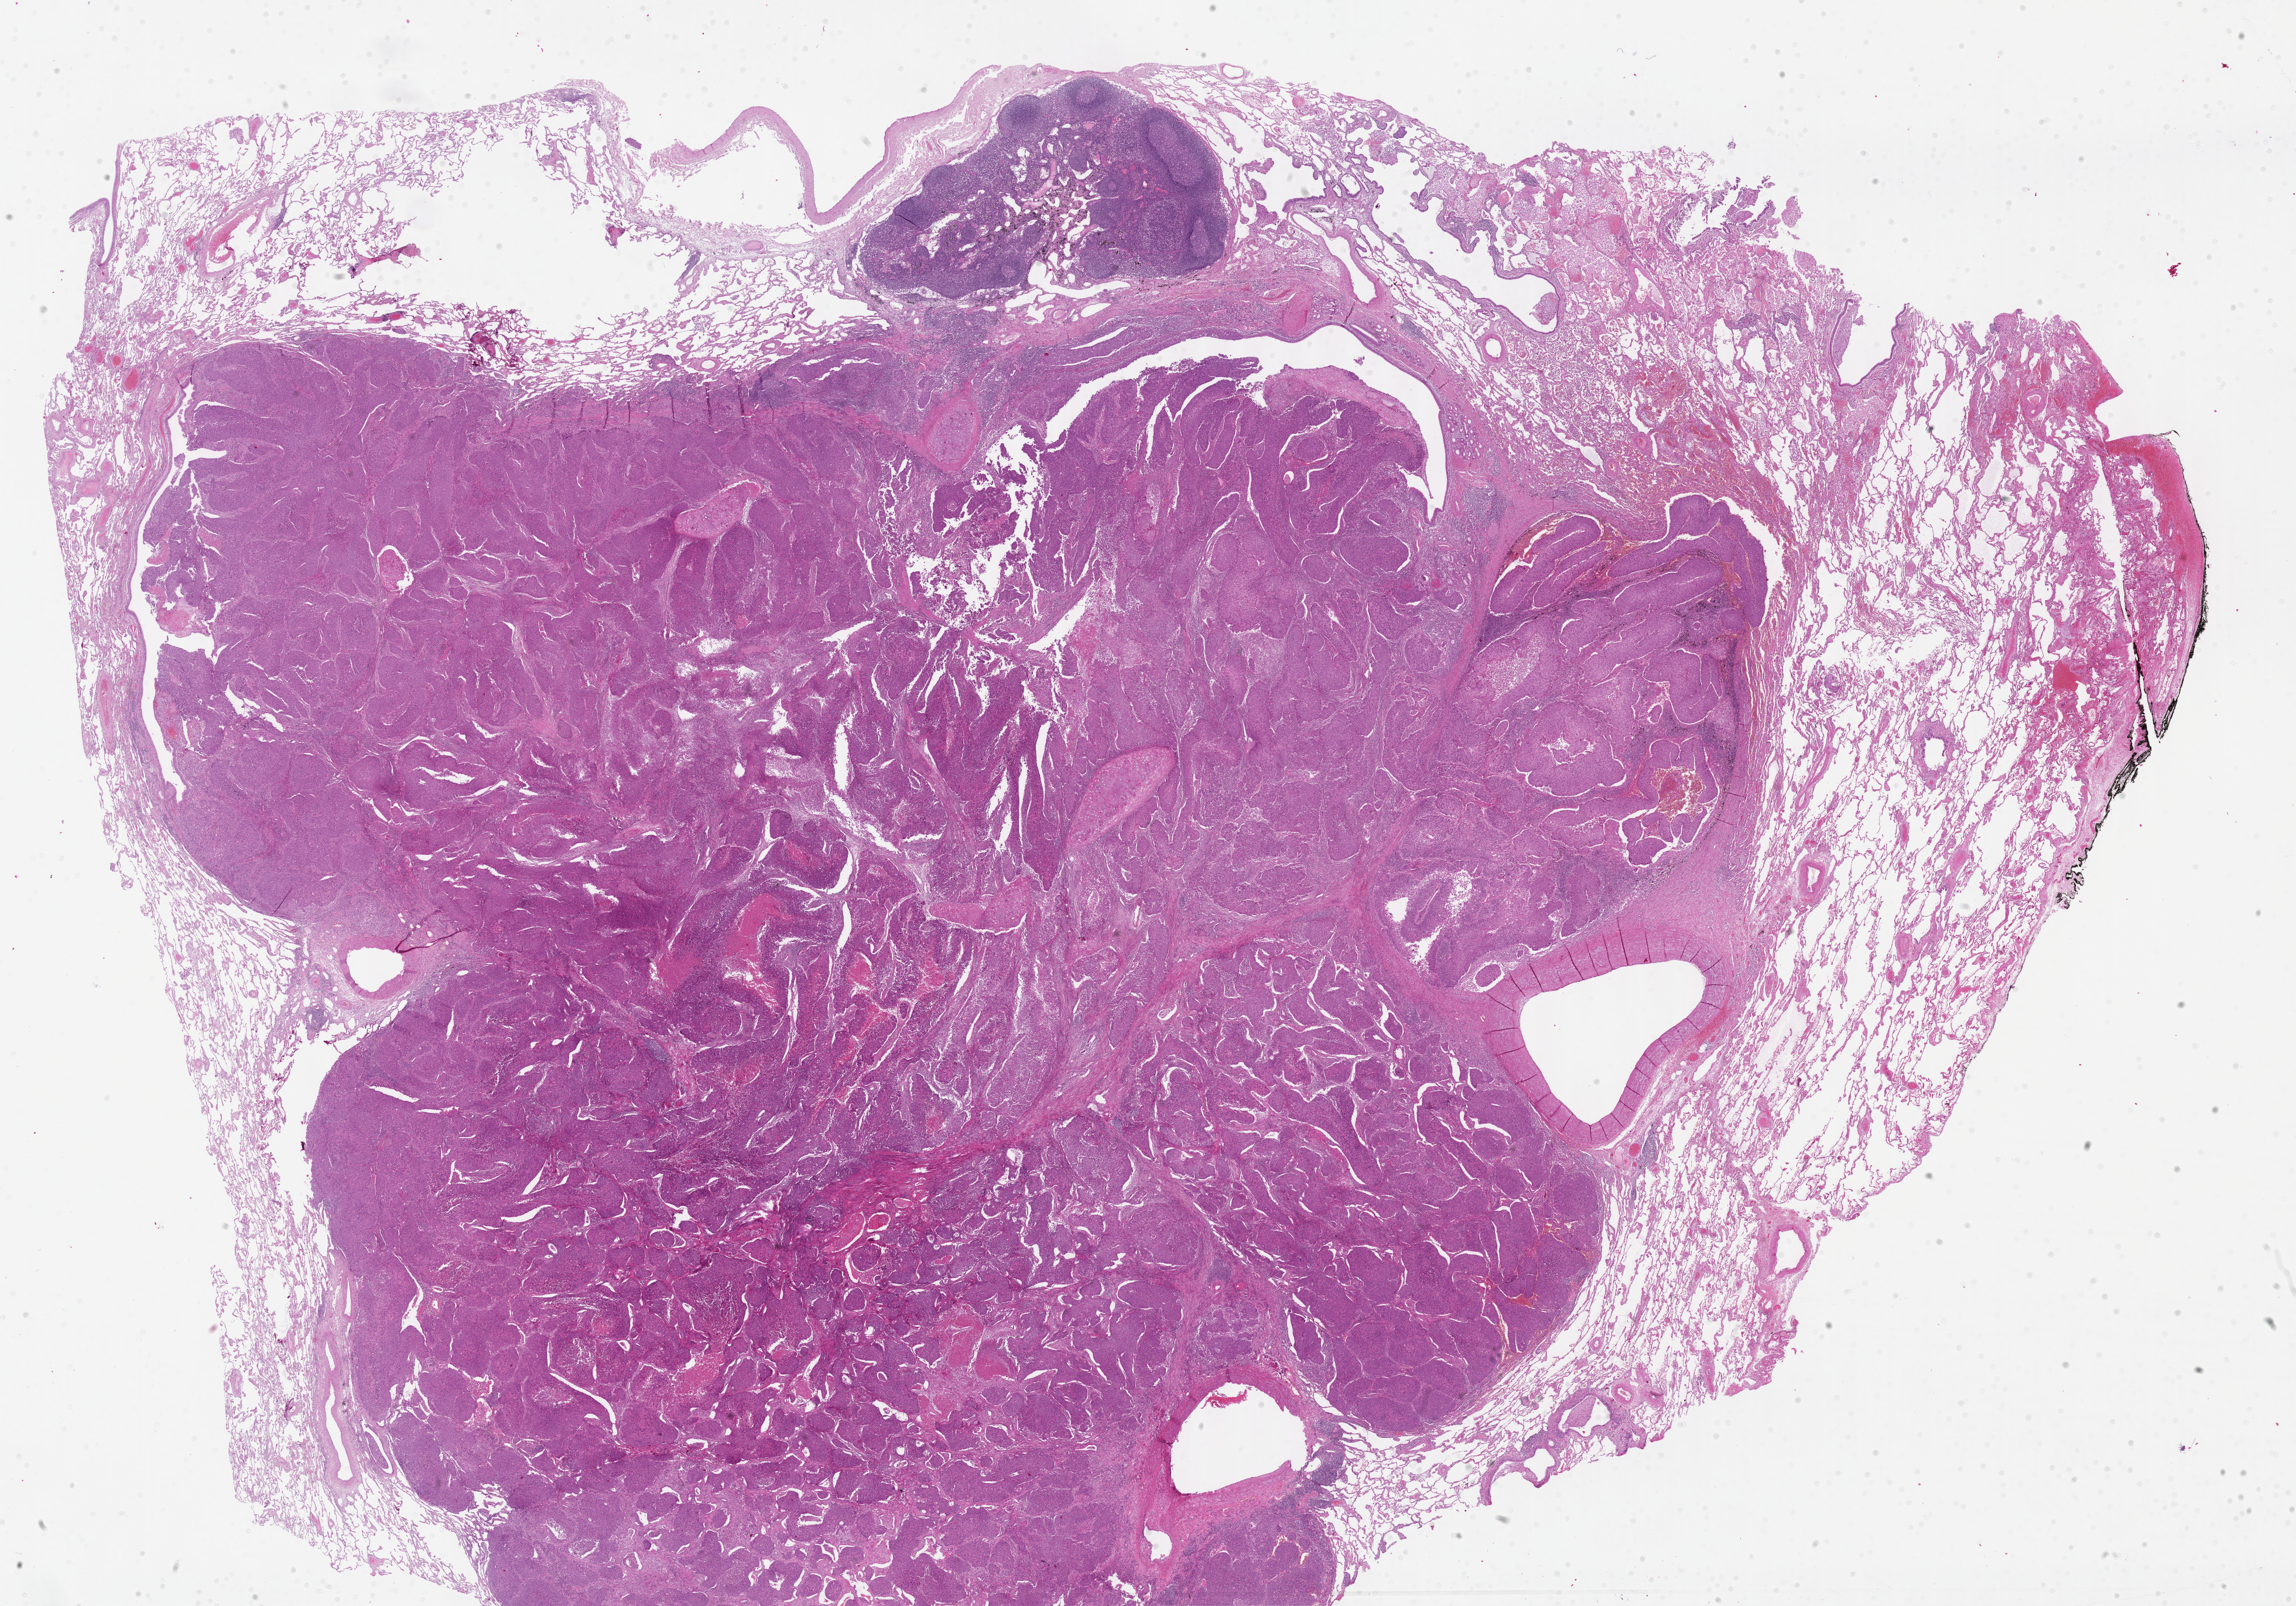
Digitized H&E tissue section (whole slide) — a low-resolution overview of the entire scanned area, about 31.7 x 22.2 mm (slide scanned at 40x). Formalin-fixed paraffin-embedded (FFPE) diagnostic section. Sample: primary tumour, lung. Female patient; age at initial diagnosis 75 years.
* laterality: right
* diagnosis: Basaloid squamous cell carcinoma (lower lobe, lung)
* AJCC pathologic stage: IIA (7th edition)